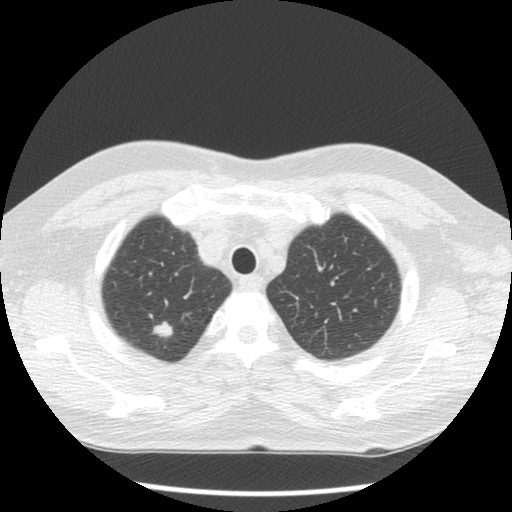
Low-dose screening chest CT, one axial slice; reconstruction kernel STANDARD; 120 kVp; lung window (W 1500 / L -600 HU); 2.5 mm slice thickness; 512 × 512 image matrix, field of view 332 × 332 mm.
Structures marked on this image (manually delineated by an expert):
- lesion 1 (tumor, upper lobe of right lung): box from (x=153, y=321) to (x=173, y=337) px